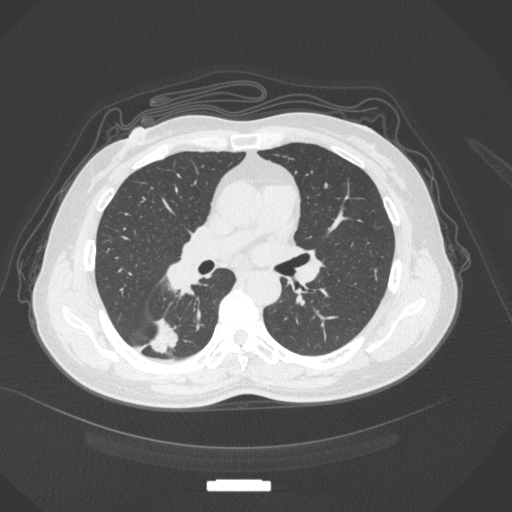
Chest CT, one axial slice; position 169 of 352 along the scan axis; 120 kVp; lung window (W 1500 / L -600 HU); 1 mm slice thickness; 512 × 512 image matrix, field of view 400 × 400 mm. Female patient, age 55 years. From the clinical record (not read from this slice): clinical TNM (as recorded): T1c N1 M0.
Annotated regions visible in this slice (rectangle marked by the reading radiologist):
- lung tumour (recorded histology: adenocarcinoma): box from (x=148, y=314) to (x=184, y=354) px